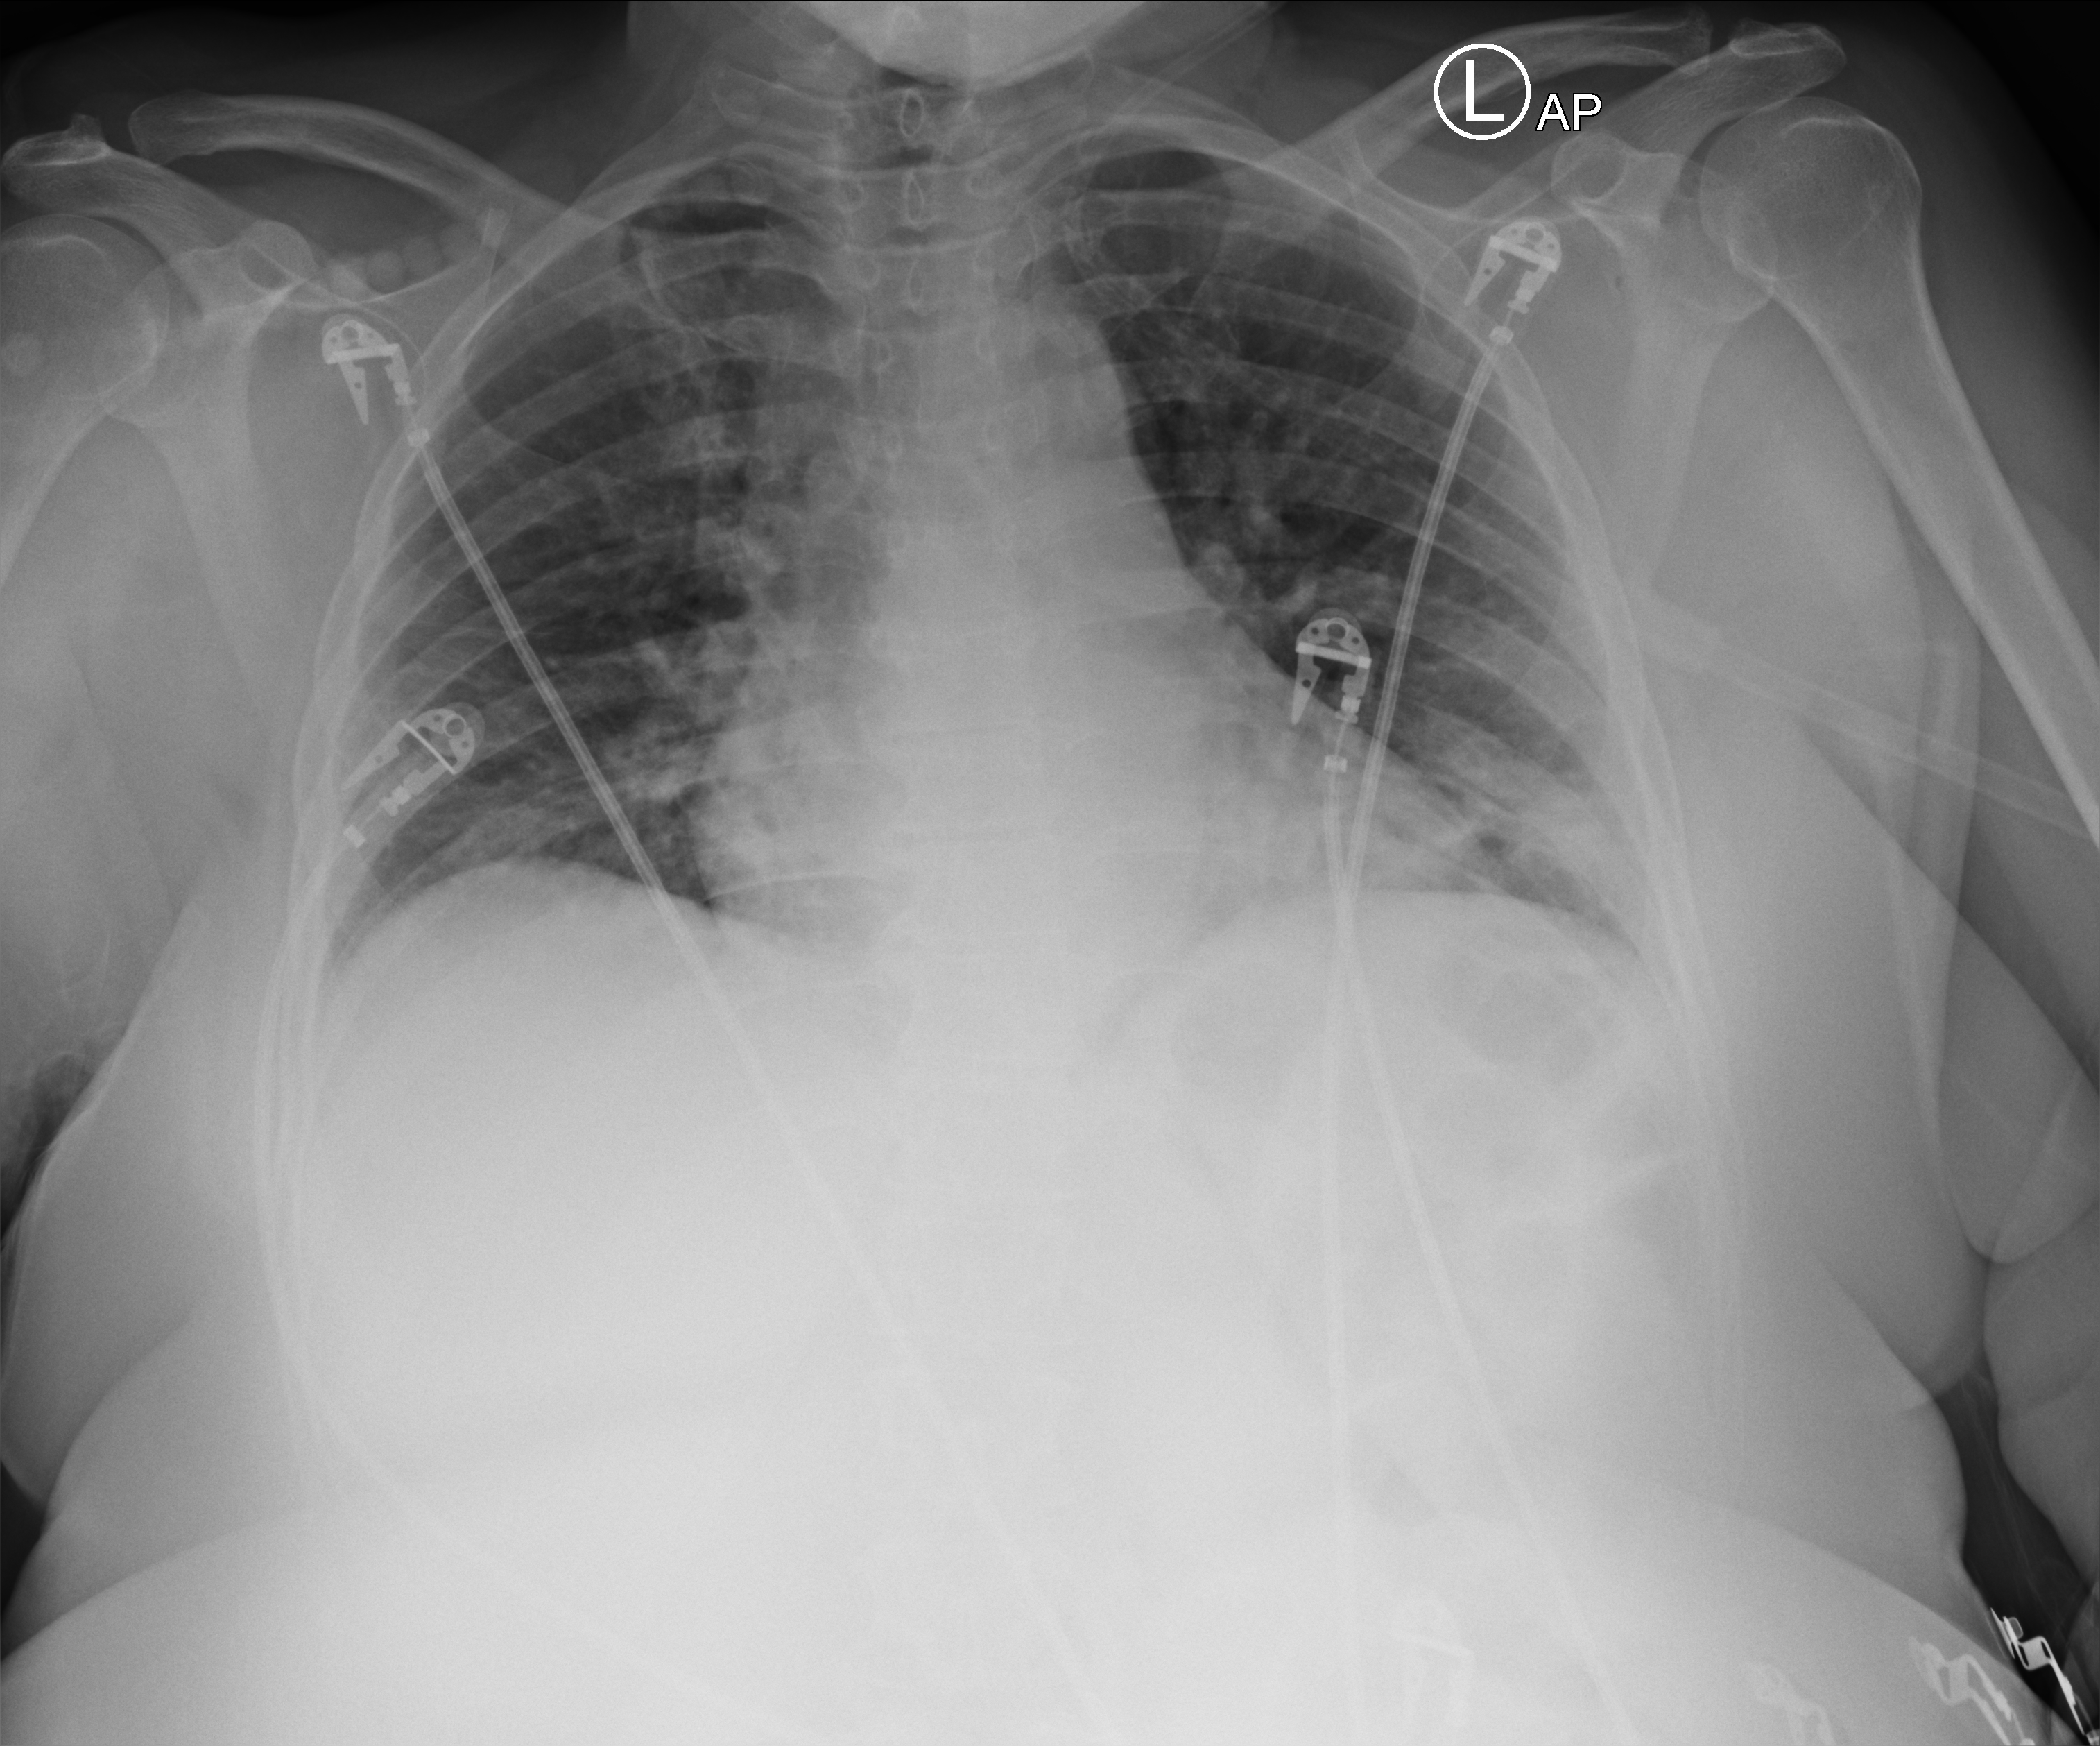
Chest X-ray (portable), anteroposterior (AP) projection. Female patient hospitalised with COVID-19, age 18–59 years.
Hospital-stay facts (about this admission, not read from this image; timing relative to this image not recorded): diabetes (admission record): no; admitted to intensive care during this hospital stay: yes.